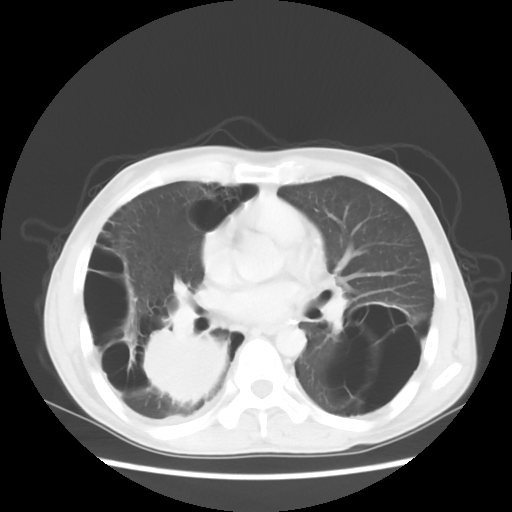
Chest CT, one axial slice. Slice 27 of 56 in the series (ordered by position). Reconstruction kernel STANDARD. 140 kVp. Lung window (W 1500 / L -600 HU). 5 mm slice thickness. 512 × 512 image matrix, field of view 351 × 351 mm. Male patient, age 41 years. From the clinical record (not read from this slice): clinical TNM (as recorded): T4 N0 M1a.
Structures marked on this image (rectangle marked by the reading radiologist):
- lung tumour (recorded histology: large cell carcinoma): bounding box [x1, y1, x2, y2] px = [146, 322, 223, 404]